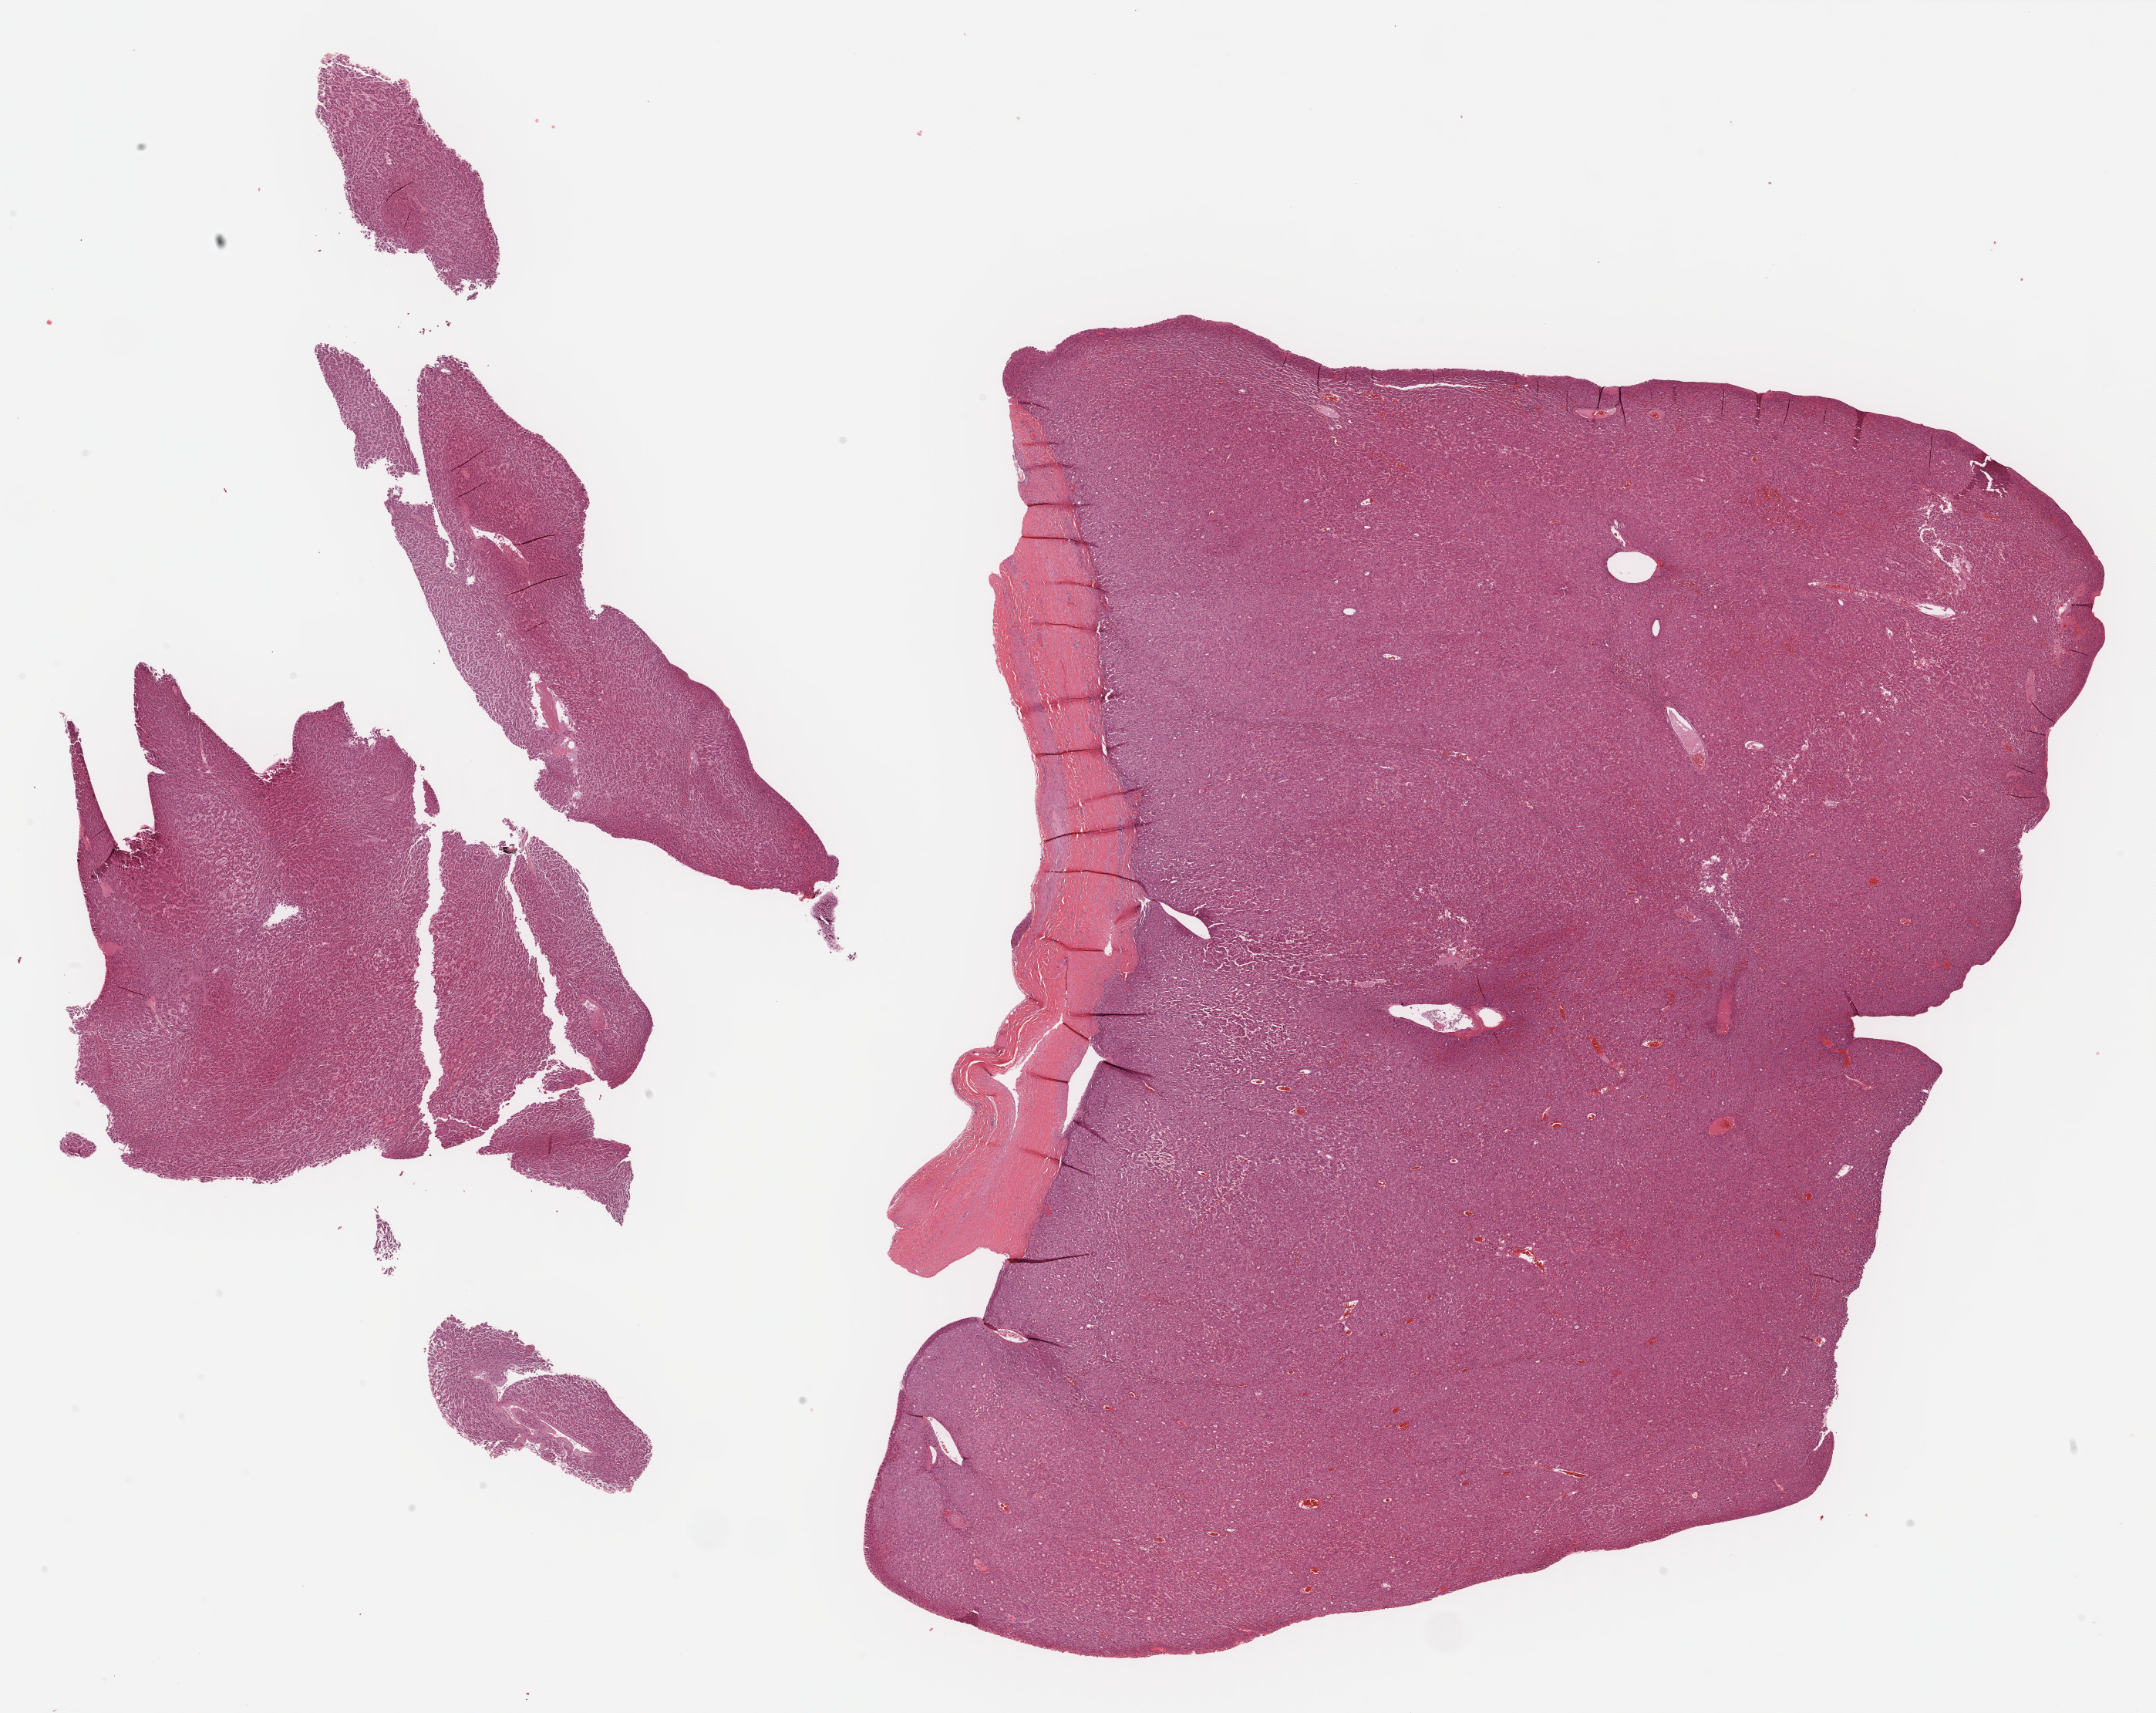
Whole-slide histology image, H&E, low-resolution overview of the scanned area, about 22.6 x 18.0 mm (from a 40x scan), formalin-fixed paraffin-embedded (FFPE) diagnostic section, sample: primary tumour, liver. Male, age 32 years at initial diagnosis. Histologic grade: G3 (poorly differentiated).
Histologic diagnosis: Hepatocellular carcinoma, NOS. AJCC pathologic stage: I.